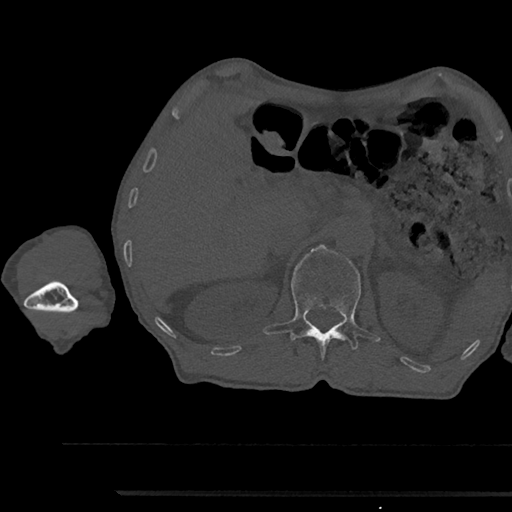
CT including the spine, one axial slice. Slice 645 of 797 in the series (ordered by position). Reconstruction kernel Br40s/3. Bone window (W 1800 / L 400 HU). 0.5 mm slice thickness. 512 × 512 image matrix, field of view 367 × 367 mm. Male patient, age 79 years. Case-level facts recorded for this patient, not image findings: primary cancer: prostate.
Structures marked on this image (semi-automatic segmentation, software-assisted and operator-edited):
- L1 vertebra: bounding box (x1, y1, x2, y2) in pixels: (263, 244, 379, 358)